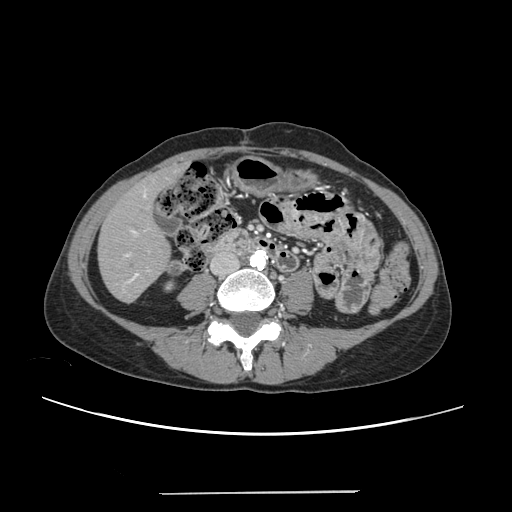
Contrast-enhanced abdominal CT, one axial slice. Slice 58 of 240 in the series (ordered by position). Intravenous contrast given. Soft-tissue window (W 400 / L 40 HU). 1.25 mm slice thickness. 512 × 512 image matrix, field of view 371 × 371 mm. Female patient, age 60 years. From the clinical record (not read from this slice): diagnosis: colorectal cancer liver metastases, imaged before liver resection; multiple liver metastases: no; largest metastasis: 1.5 cm; chemotherapy before resection: yes.
Annotated regions visible in this slice (manually delineated by an expert):
- liver: bounding box (x1, y1, x2, y2) in pixels: (99, 168, 180, 301)
- planned liver remnant (the part of the liver to remain after resection): (99, 172, 171, 301)
- portal vein (with intrahepatic branches): (125, 188, 147, 283)